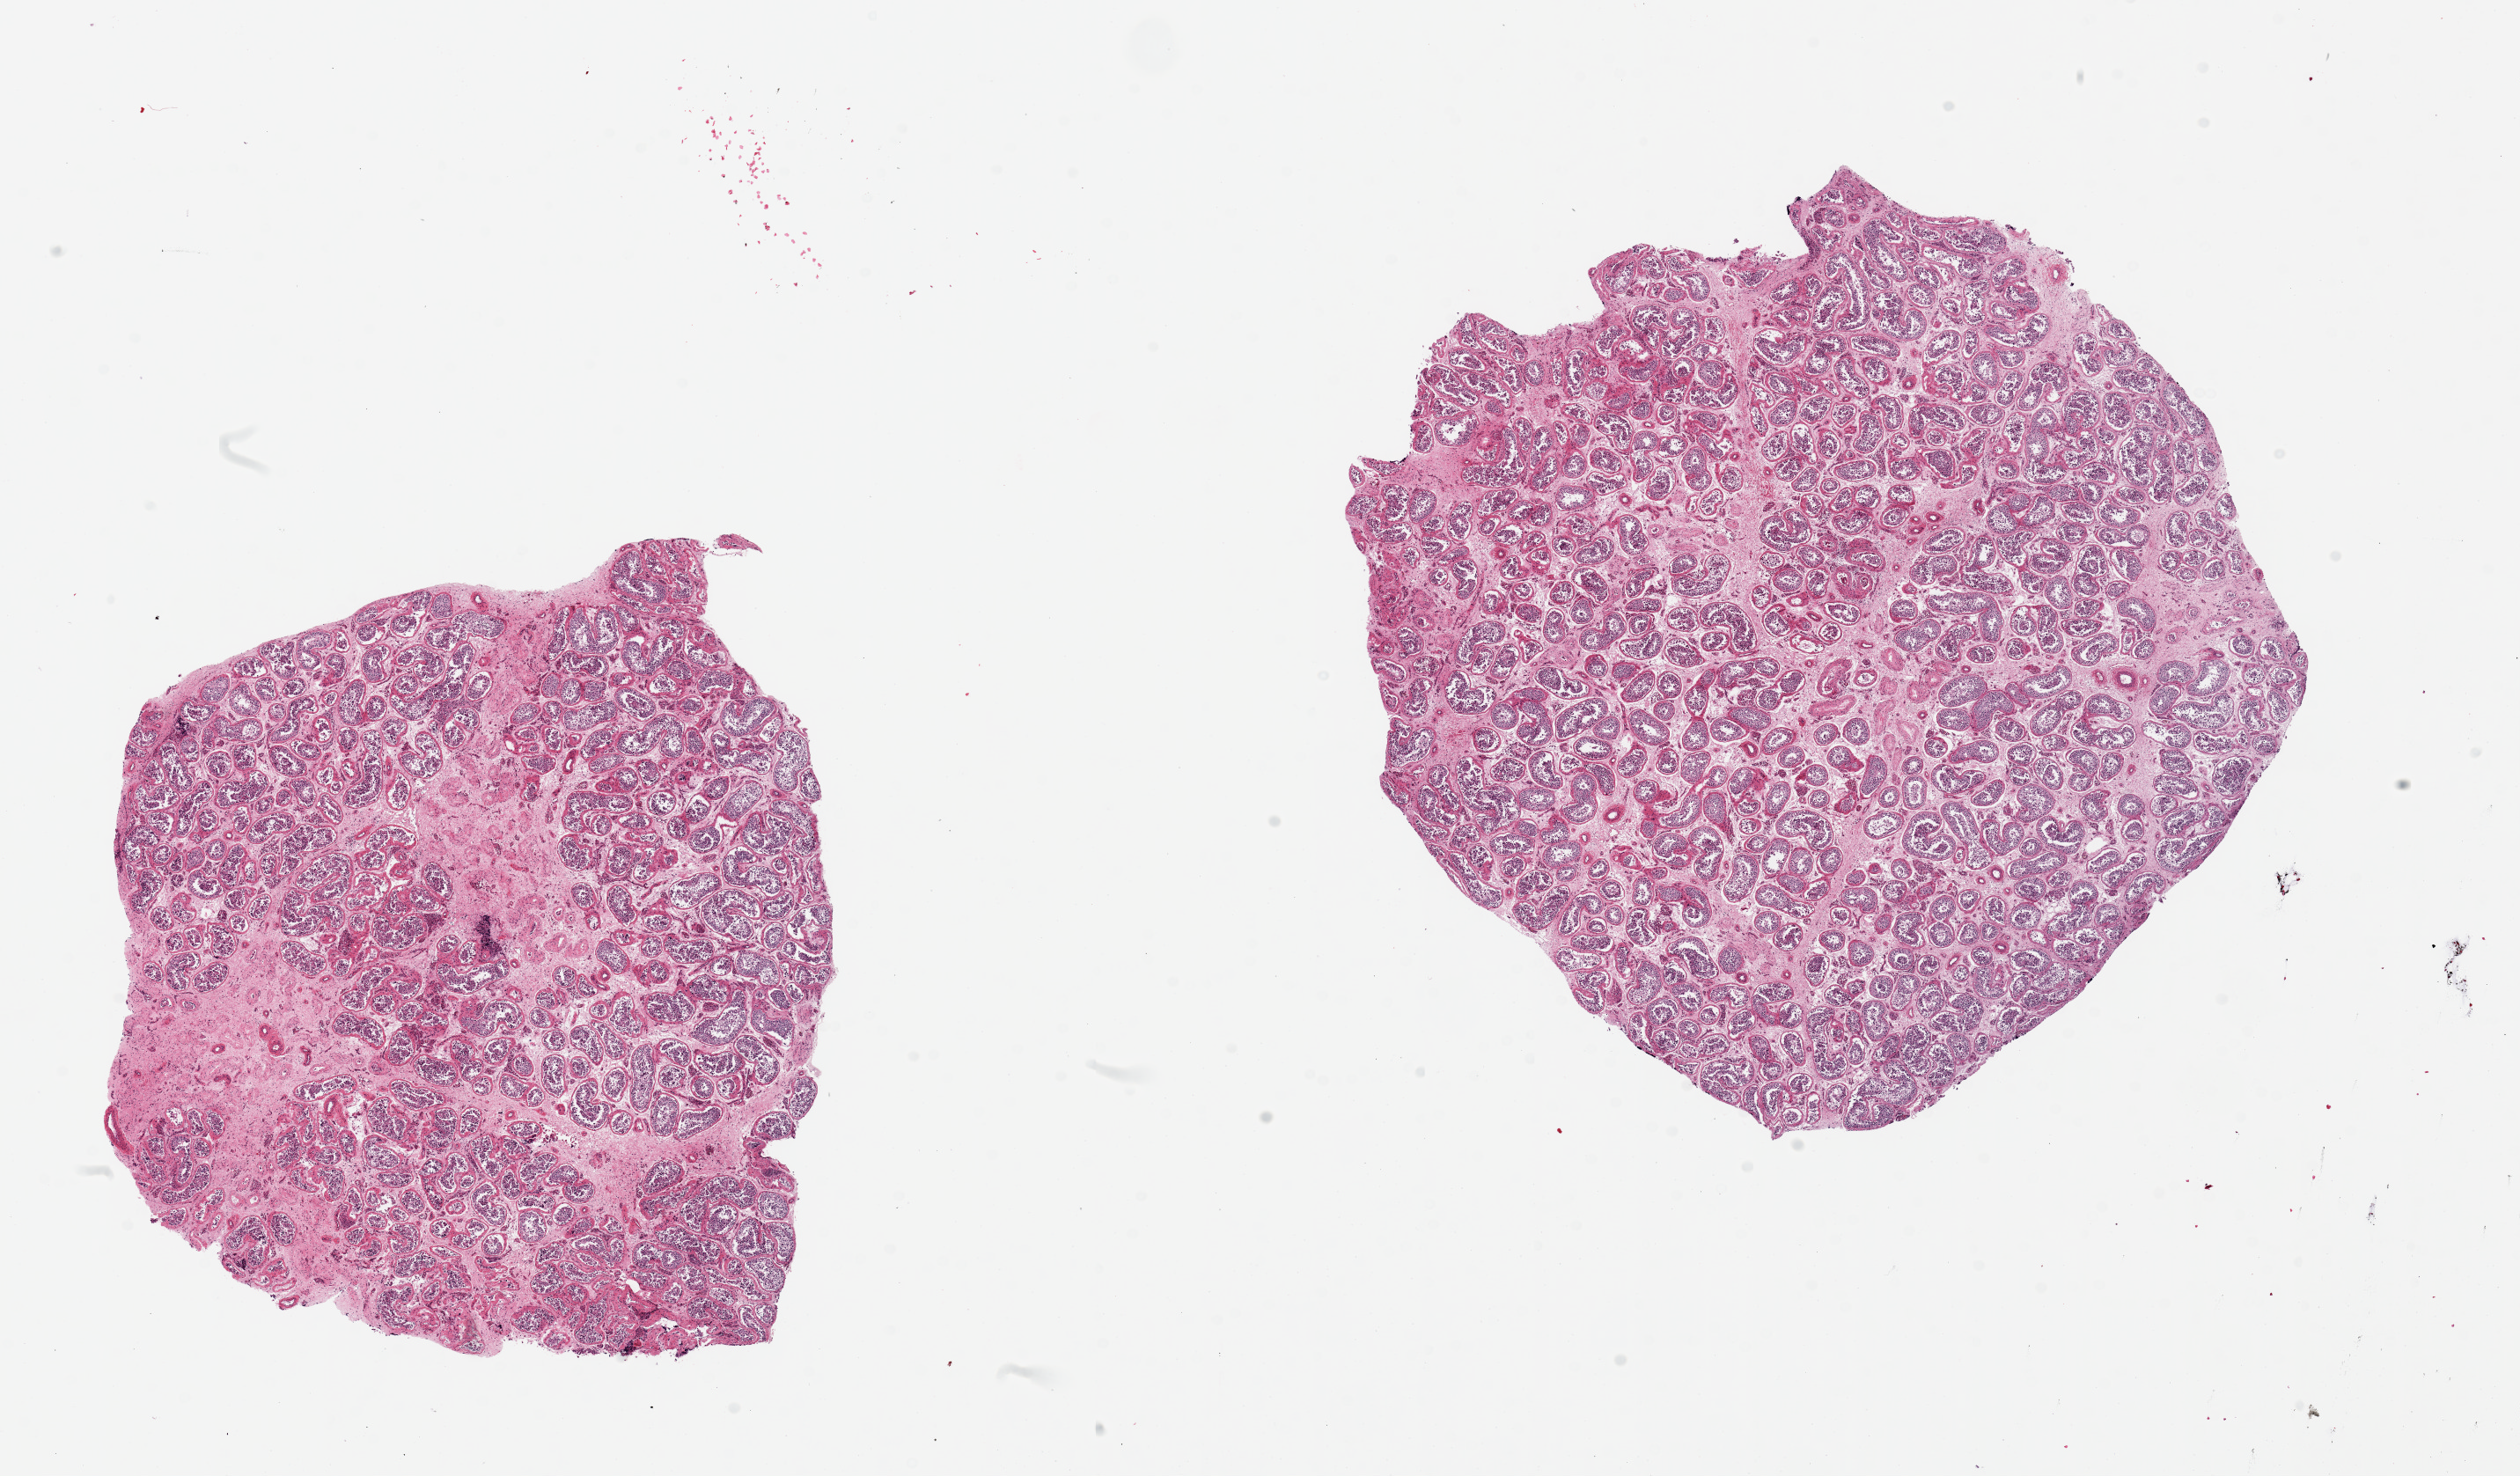
Whole-slide image, H&E stain, a low-resolution overview of the entire scanned area, about 22.6 x 13.3 mm, PAXgene-fixed, paraffin-embedded tissue, section of testis (target tissue), tissue donor sample.
• pathologist's review note for this sample: 2 pieces, 8x6 & 8x7mm; Moderate tubular and interstitial fibrosis; decreased spermatogenesis